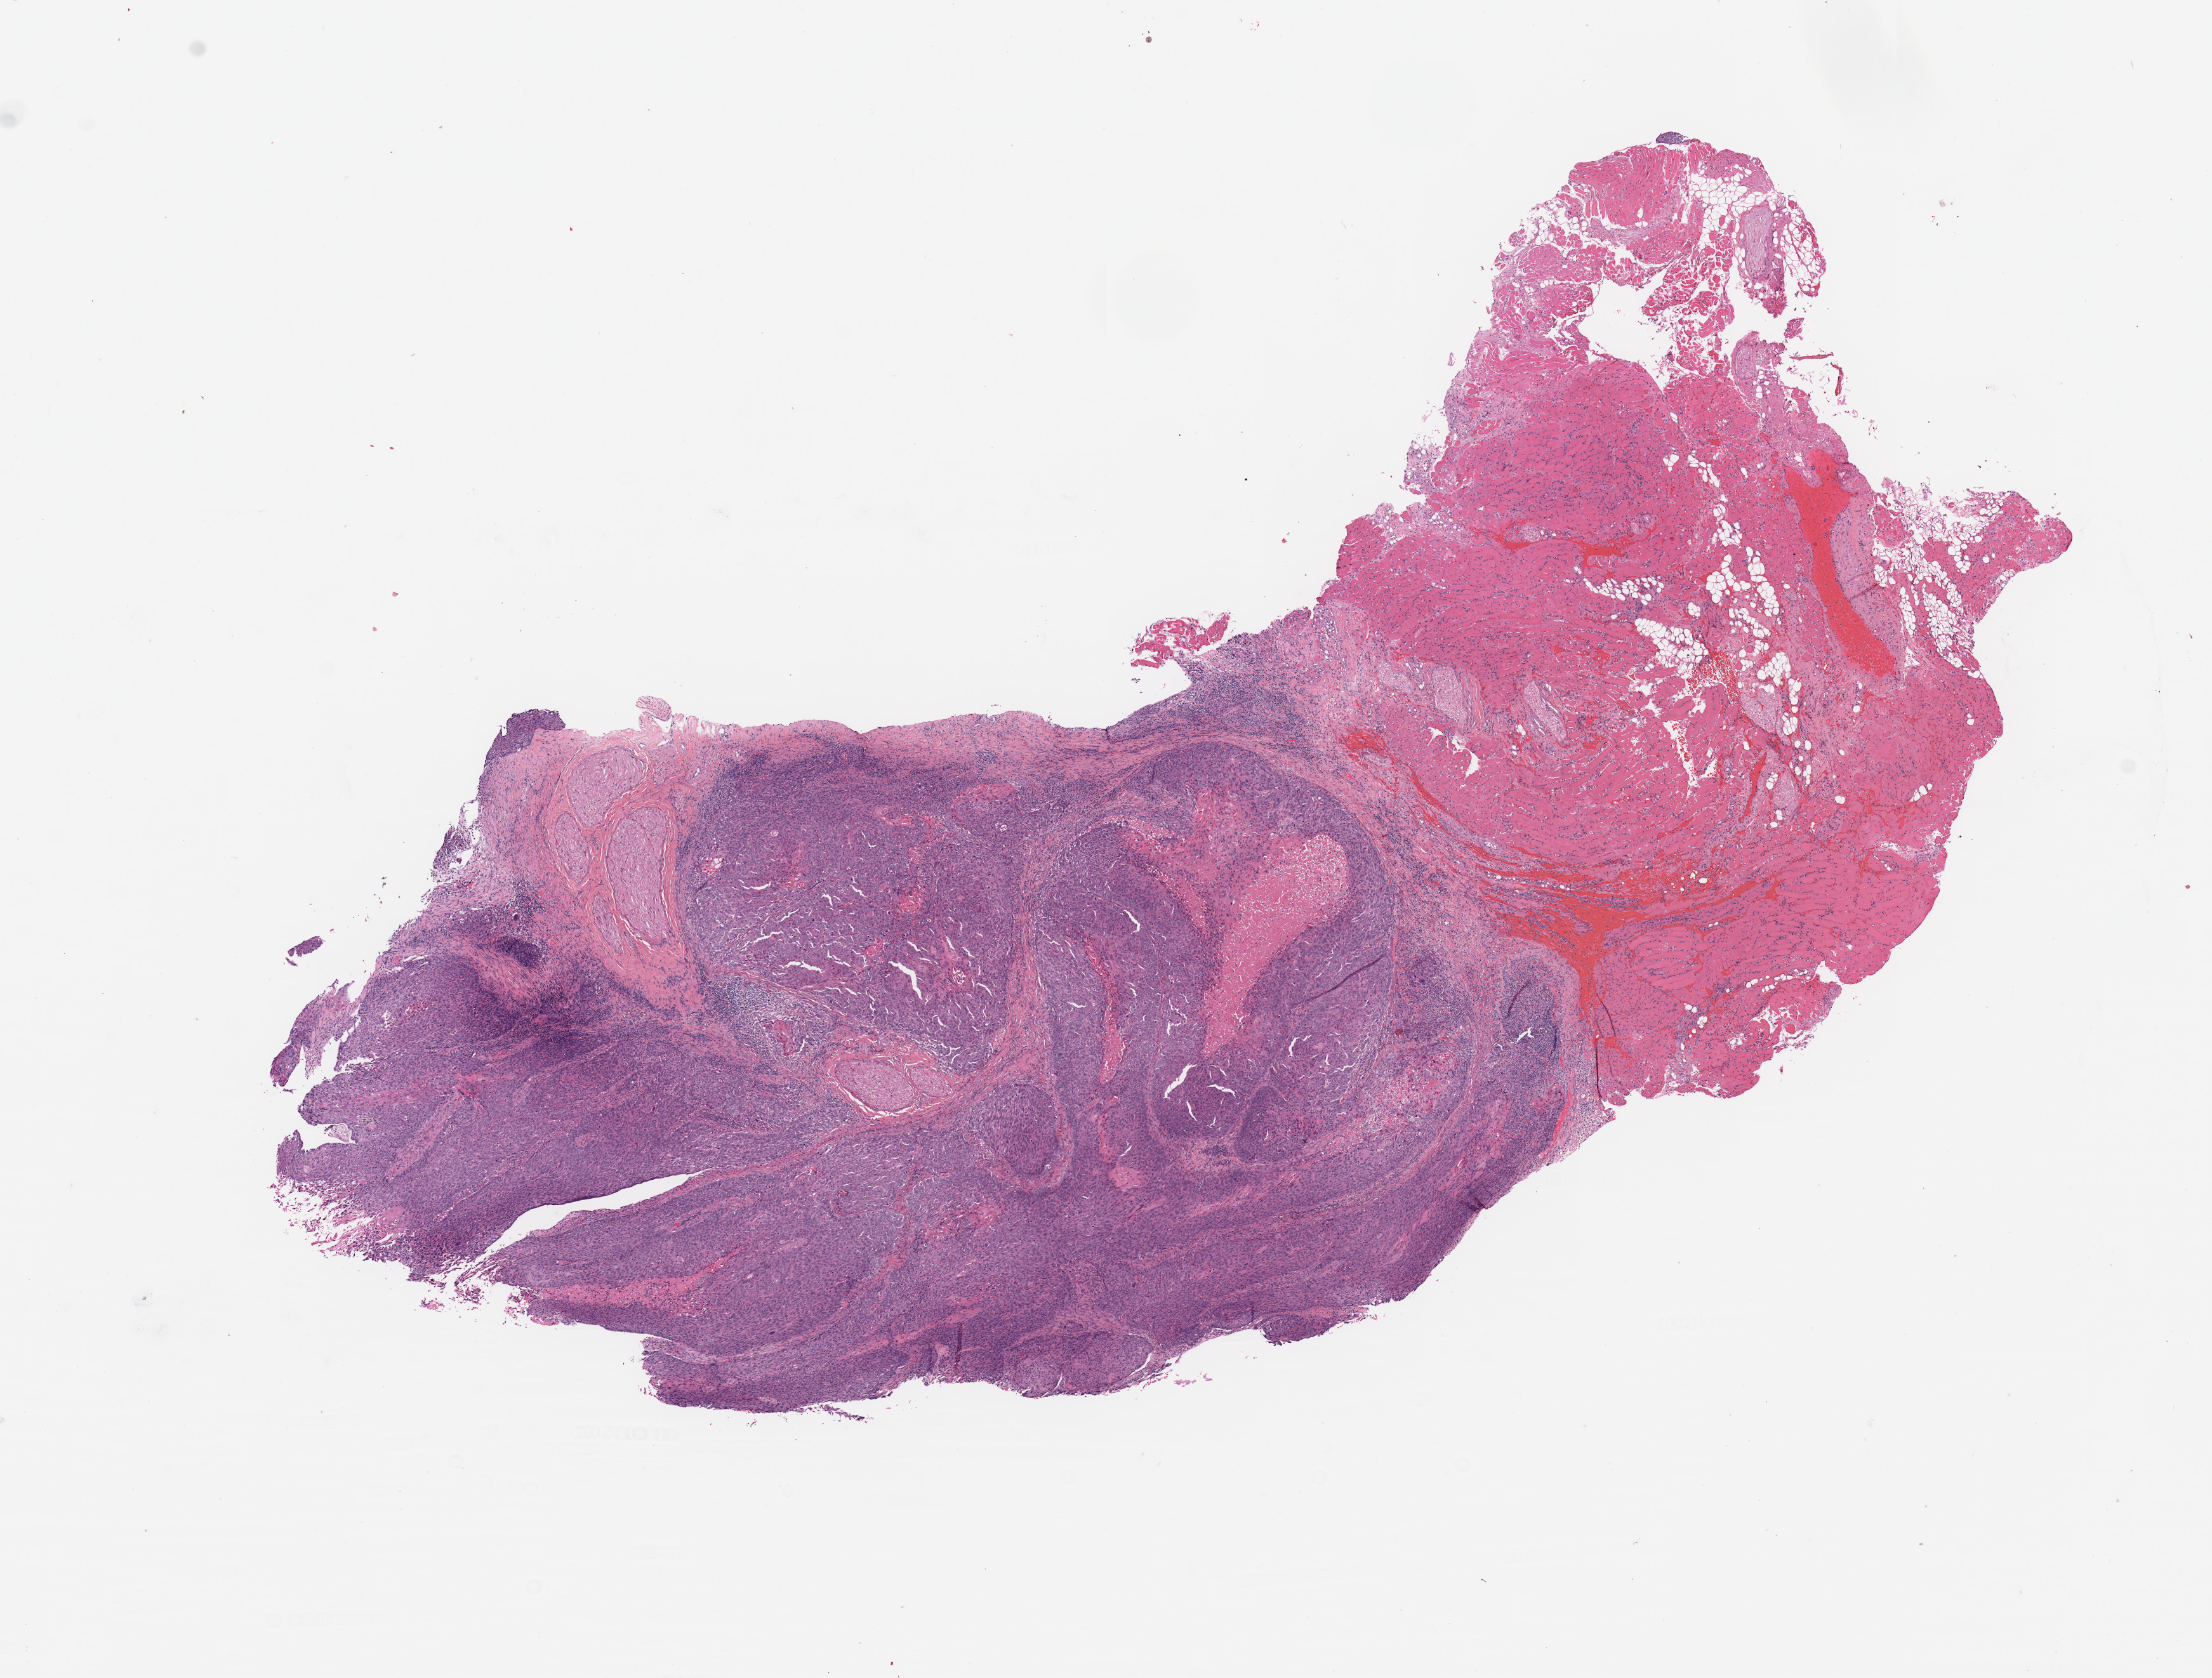
Digitized Hematoxylin and eosin (H&E) stained tissue section (whole slide) — low-resolution overview of the scanned area, about 13.8 x 10.5 mm, tumour tissue sample, sampled site: oral cavity. Patient: male, age 54 years. Histologic grade: G2 (moderately differentiated). Composition of this section per pathologist review: tumour nuclei 80%, necrosis 5%.
• histologic diagnosis: Squamous cell carcinoma, NOS (overlapping lesion of lip, oral cavity and pharynx)
• AJCC pathologic stage: IVA
• primary tumour site (as recorded): oral cavity